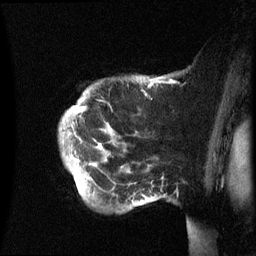
Breast MRI (dynamic contrast-enhanced), one sagittal slice; slice 50 of 60 in the series (ordered by position); dynamic contrast-enhanced series, image 2 of 3 at this slice position (ordered by acquisition); 1.5 T; TE 4.2 ms, TR 8.4 ms; 2.4 mm slice thickness; 256 × 256 image matrix. Female patient, age 49 years.
Annotated regions visible in this slice (semi-automatic segmentation, software-assisted and operator-edited):
- analysis volume of interest (the breast-tissue region the enhancement analysis was run in; not a lesion): bounding box [x1, y1, x2, y2] px = [59, 75, 169, 211]
- tumour enhancement mask (voxels above the 70 % enhancement threshold inside the analysis volume of interest): [78, 82, 160, 112]